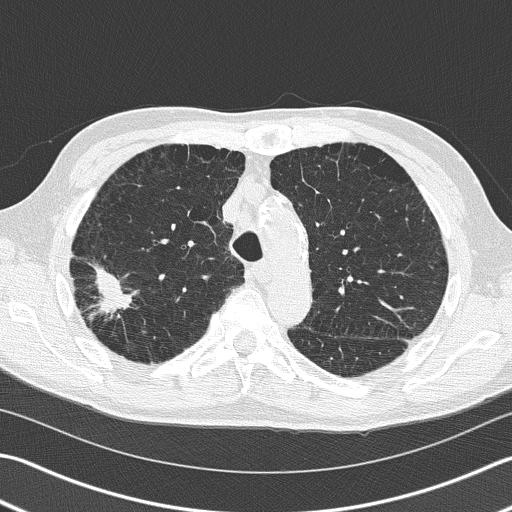
Low-dose screening chest CT, one axial slice; position 114 of 163 along the scan axis; reconstruction kernel B50f; 120 kVp; lung window (W 1500 / L -600 HU); 2 mm slice thickness; 512 × 512 image matrix, field of view 346 × 346 mm.
Annotated regions visible in this slice (expert manual segmentation):
- lesion 1 (tumor, upper lobe of right lung): bounding box <93,263,134,314> (left, top, right, bottom; pixels)